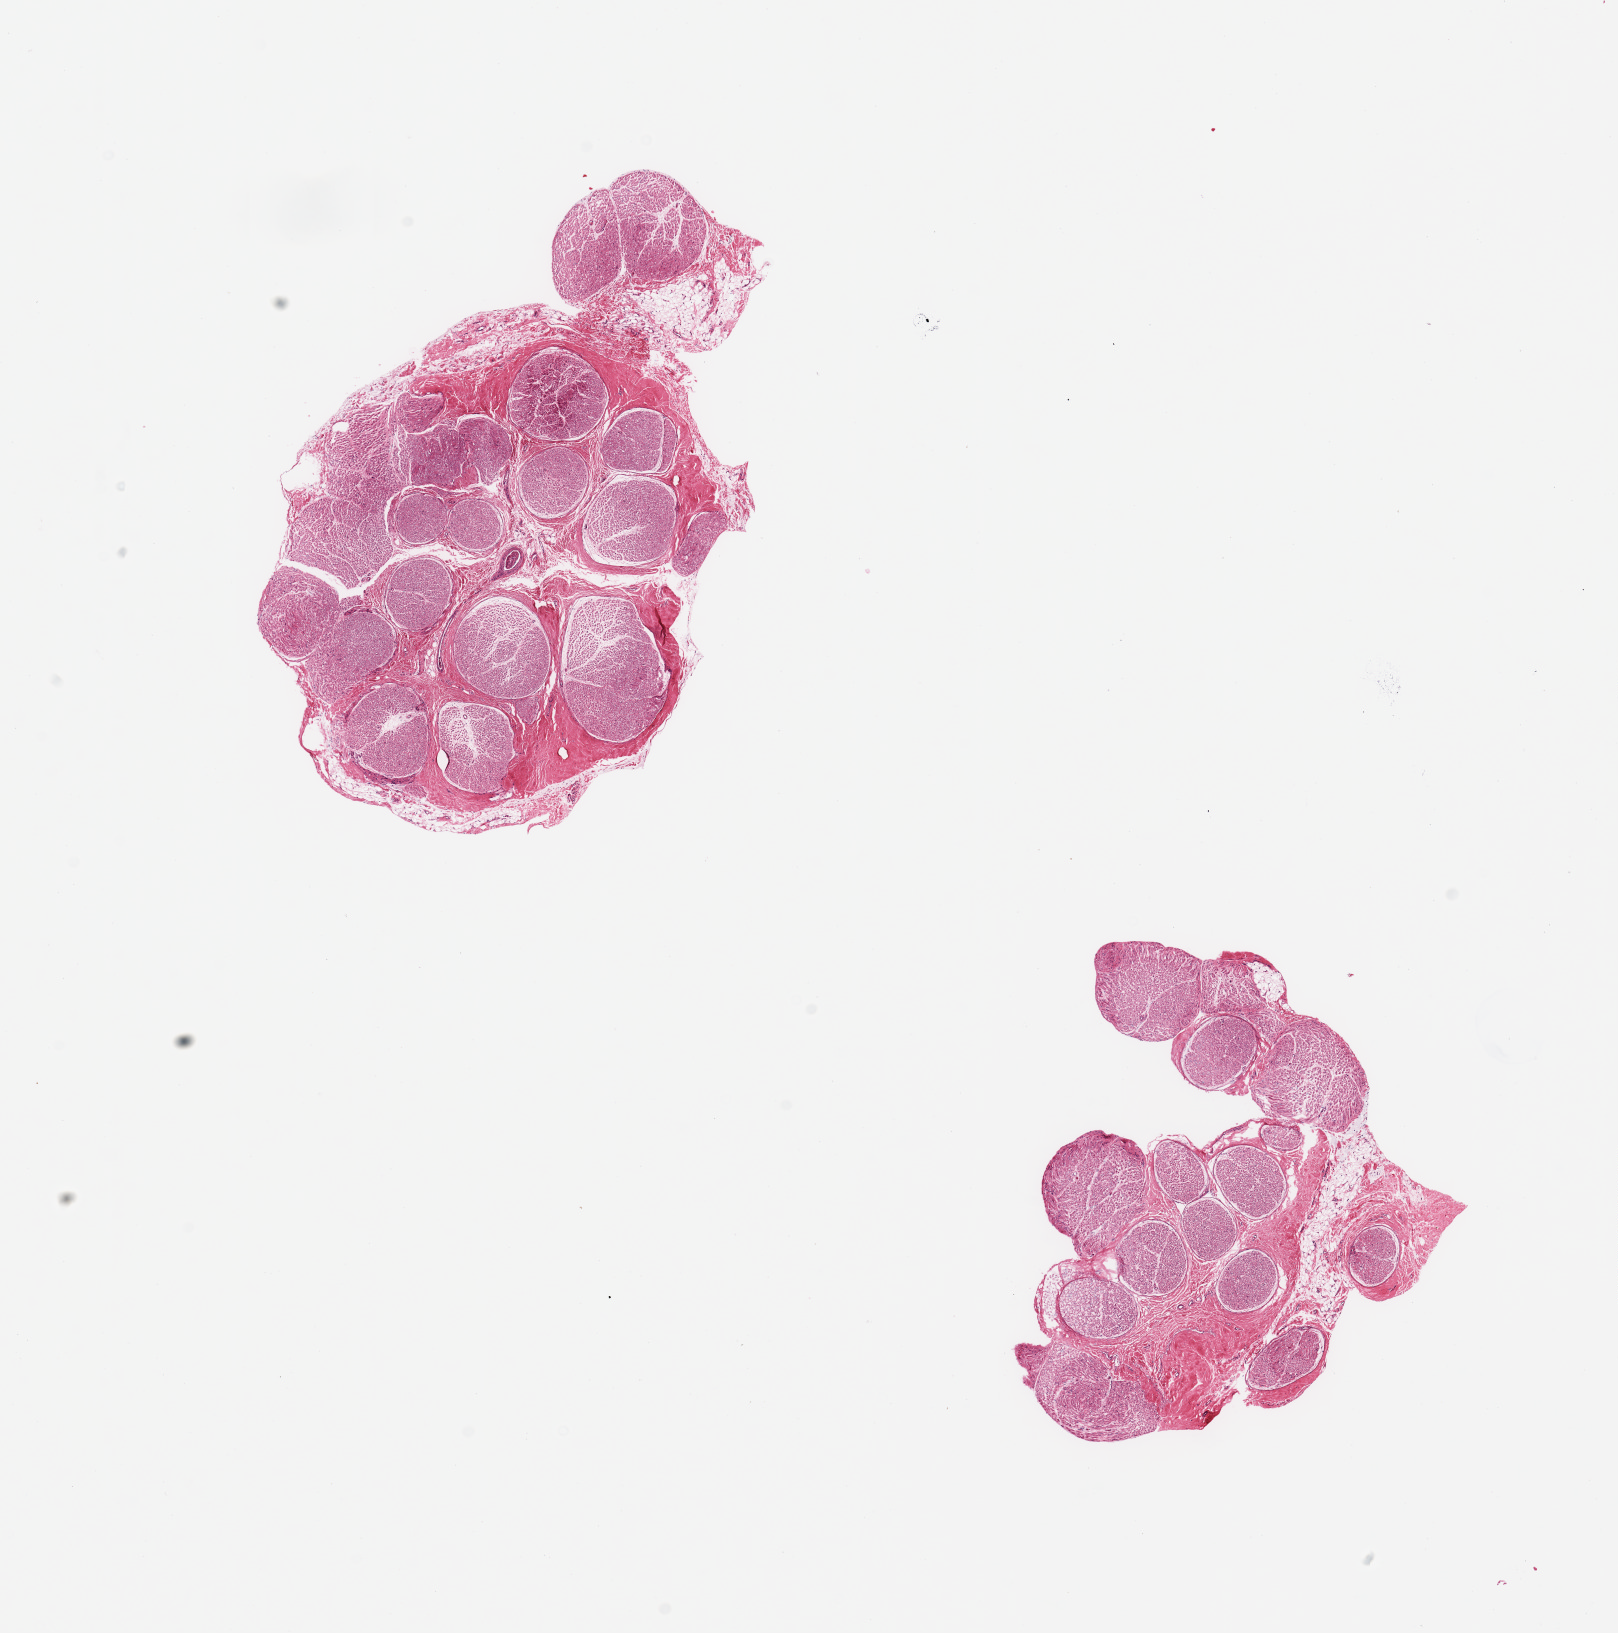
Whole-slide image, haematoxylin and eosin stain, whole scanned area (about 12.8 x 12.9 mm) shown as a low-resolution overview, PAXgene-fixed, paraffin-embedded tissue, sampled site (target tissue): tibial nerve, donor tissue sample. Donor sex: male.
Pathologist's review note for this sample: 2 pieces; well trimmed; 5 & 10% internal & external fat.